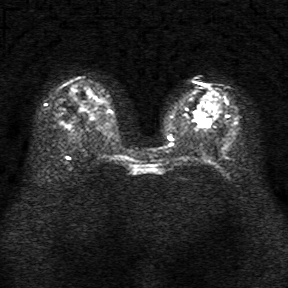
Breast MRI, one axial slice. Position 15 of 34 along the scan axis. Diffusion-weighted series; image 2 of 4 stored at this slice position (different b-values; order by instance number). 1.5 T. 288 × 288 image matrix. Female patient.
Annotated regions visible in this slice (outlined manually by an expert reader):
- tumour on diffusion-weighted imaging: bounding box (x1, y1, x2, y2) in pixels: (199, 115, 208, 126)